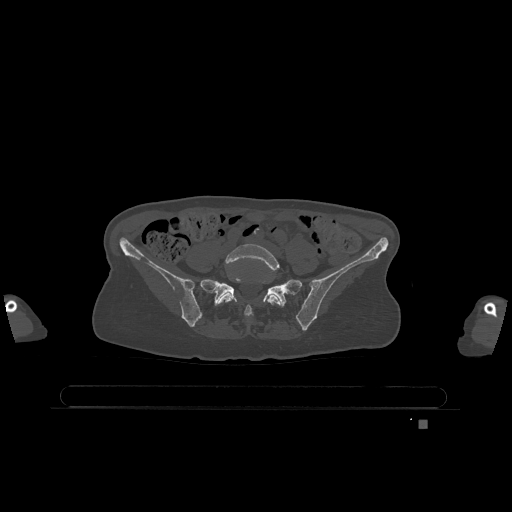
CT including the spine, one axial slice; bone window (W 1800 / L 400 HU); 0.5 mm slice thickness; 512 × 512 image matrix, field of view 500 × 500 mm. Patient: female, 74 years. Case-level facts recorded for this patient, not image findings: primary cancer: lung.
Outlined on this slice (semi-automatic segmentation, software-assisted and operator-edited):
- L5 vertebra: bounding box (x1, y1, x2, y2) in pixels: (217, 244, 282, 316)